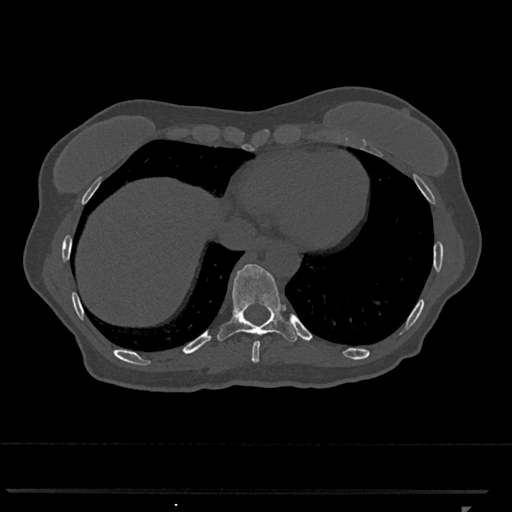
CT including the spine, one axial slice. Position 577 of 793 along the scan axis. Bone window (W 1800 / L 400 HU). 512 × 512 image matrix, field of view 380 × 380 mm. Patient: female, 62 years. Case-level facts recorded for this patient, not image findings: primary cancer: renal.
Structures marked on this image (semi-automatically segmented with operator editing):
- T10 vertebra: box from (x=217, y=264) to (x=299, y=343) px
- T9 vertebra: (x=251, y=342)–(x=260, y=363)